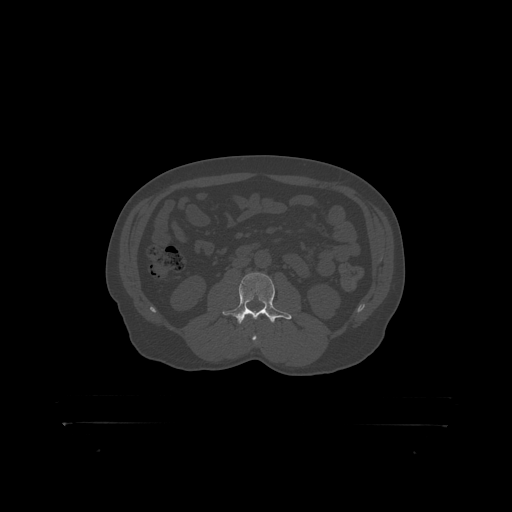
CT including the spine, one axial slice; slice 270 of 399 in the series (ordered by position); reconstruction kernel STANDARD; bone window (W 1800 / L 400 HU); 1.25 mm slice thickness; 512 × 512 image matrix, field of view 650 × 650 mm. Patient: male, 46 years. From the clinical record (not read from this slice): primary cancer: skin.
Structures marked on this image (semi-automatic segmentation, software-assisted and operator-edited):
- L3 vertebra: bounding box <228,273,282,319> (left, top, right, bottom; pixels)